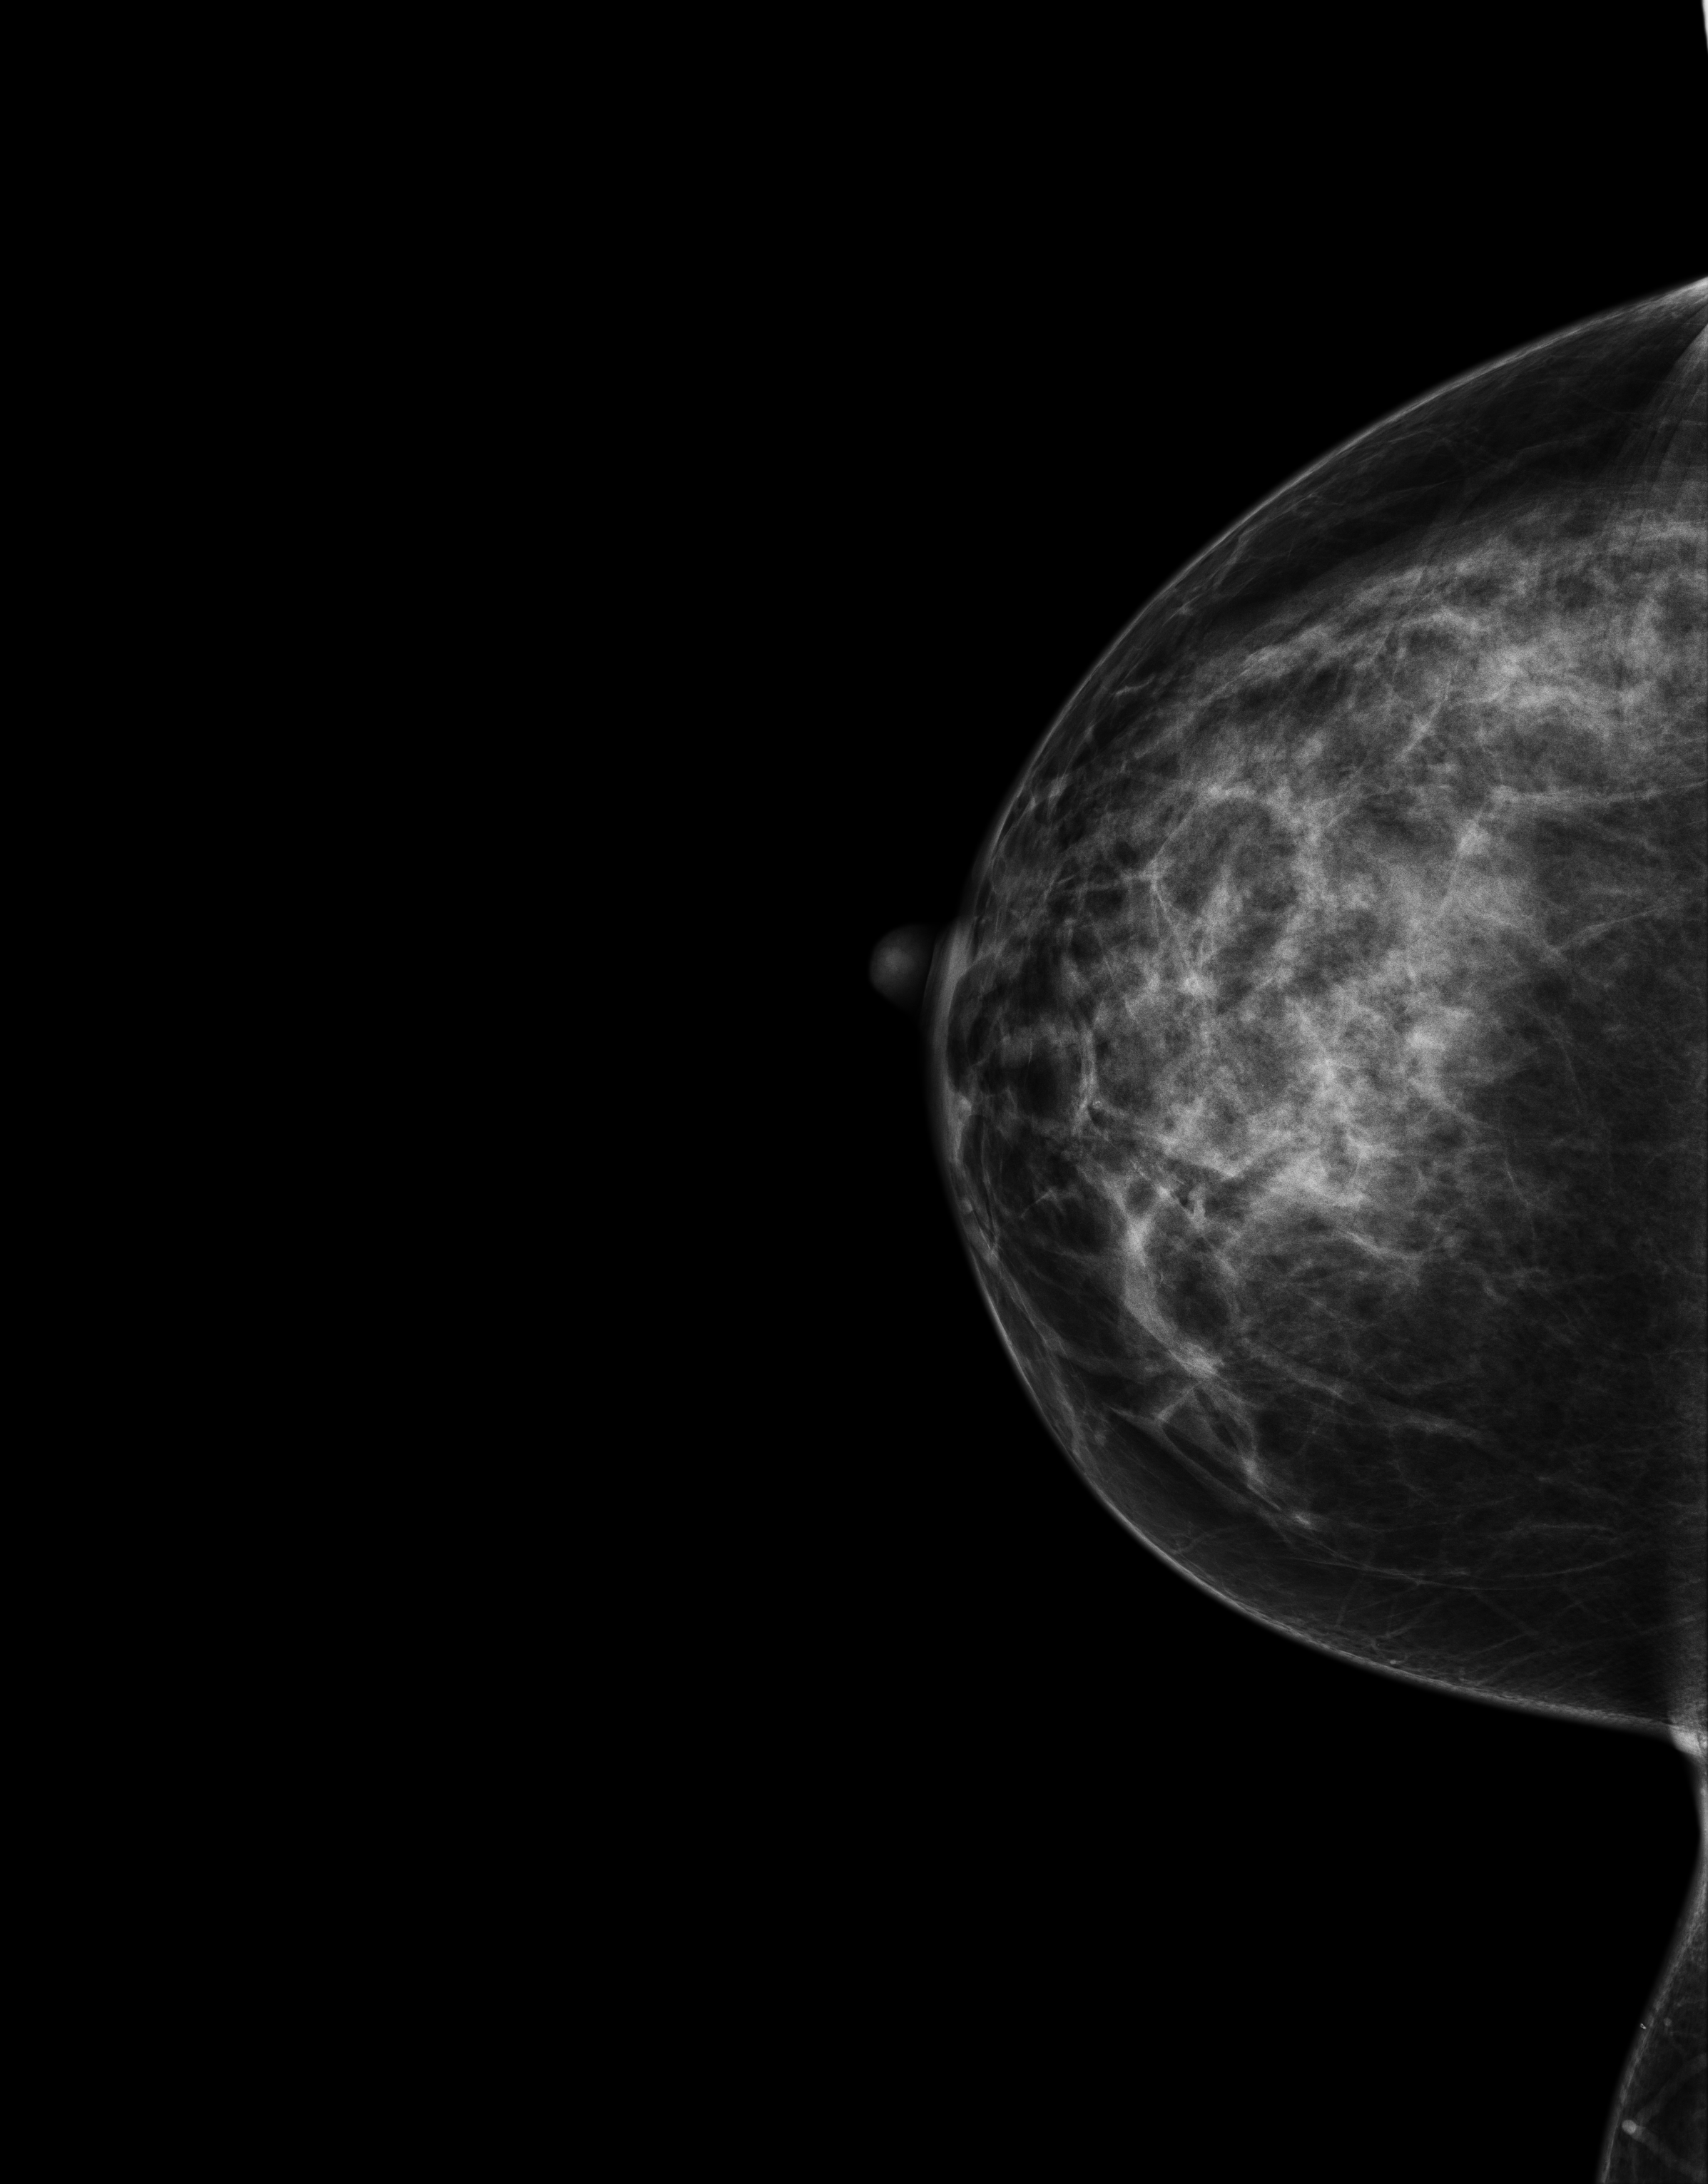
Full-field digital mammogram (FFDM); right breast; craniocaudal (CC) view; annual screening mammography examination. Female patient, age 49 years.
BI-RADS breast density category at the screening exam (both breasts, scale 1–4): 3. Final BI-RADS assessment for this screening round (tomosynthesis exam, both breasts): category 1. Recall: no recall after this screen.